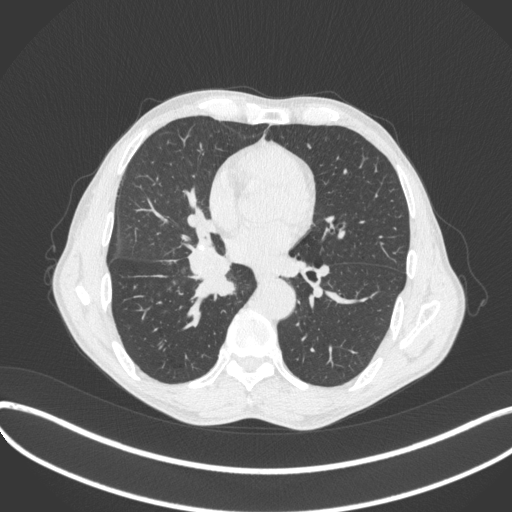
Chest CT, one axial slice. Reconstruction kernel B31f. Lung window (W 1500 / L -600 HU). 1 mm slice thickness. 512 × 512 image matrix, field of view 400 × 400 mm. Male patient, age 65 years. Case-level facts recorded for this patient, not image findings: clinical TNM (as recorded): T2a N0 M0.
Annotated regions visible in this slice (bounding box drawn by a radiologist):
- lung tumour (recorded histology: squamous cell carcinoma): bounding box [x1, y1, x2, y2] px = [186, 240, 241, 298]